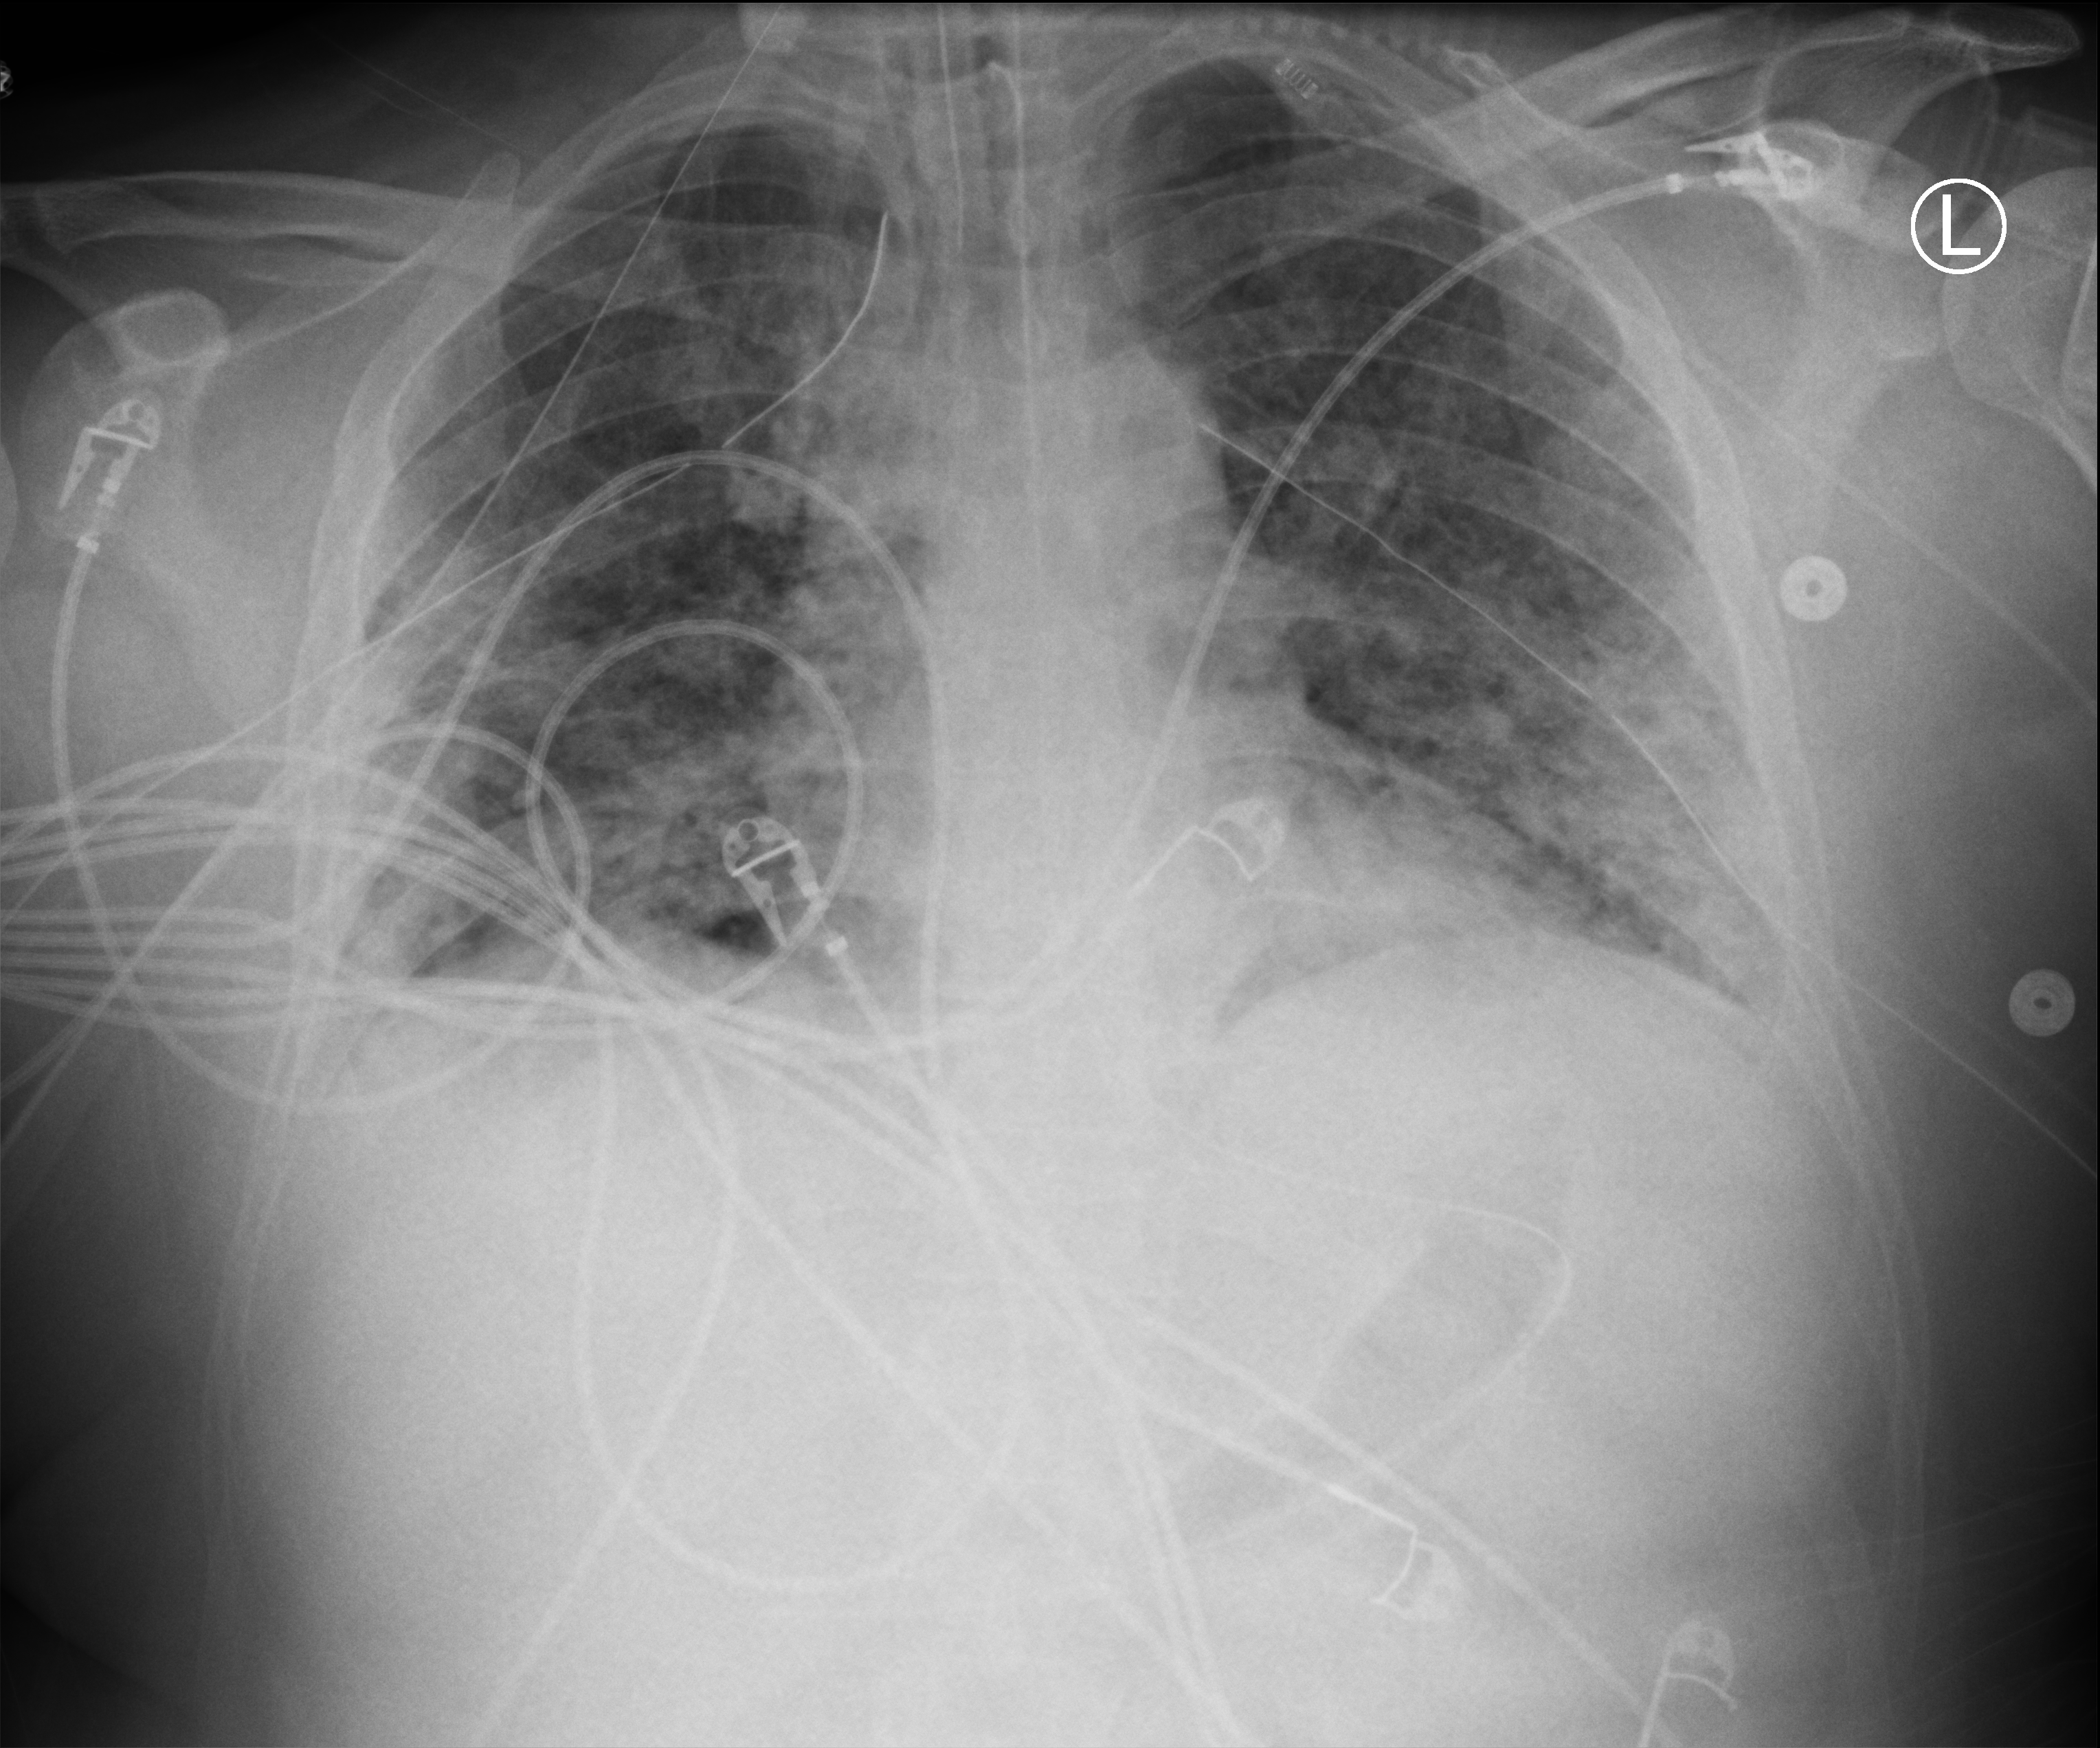
Chest X-ray (portable), anteroposterior (AP) projection. Patient hospitalised with COVID-19; male, aged 18–59 years.
Hospital-stay facts (about this admission, not read from this image; timing relative to this image not recorded):
- admitted to intensive care during this hospital stay: yes
- mechanically ventilated during this hospital stay: yes